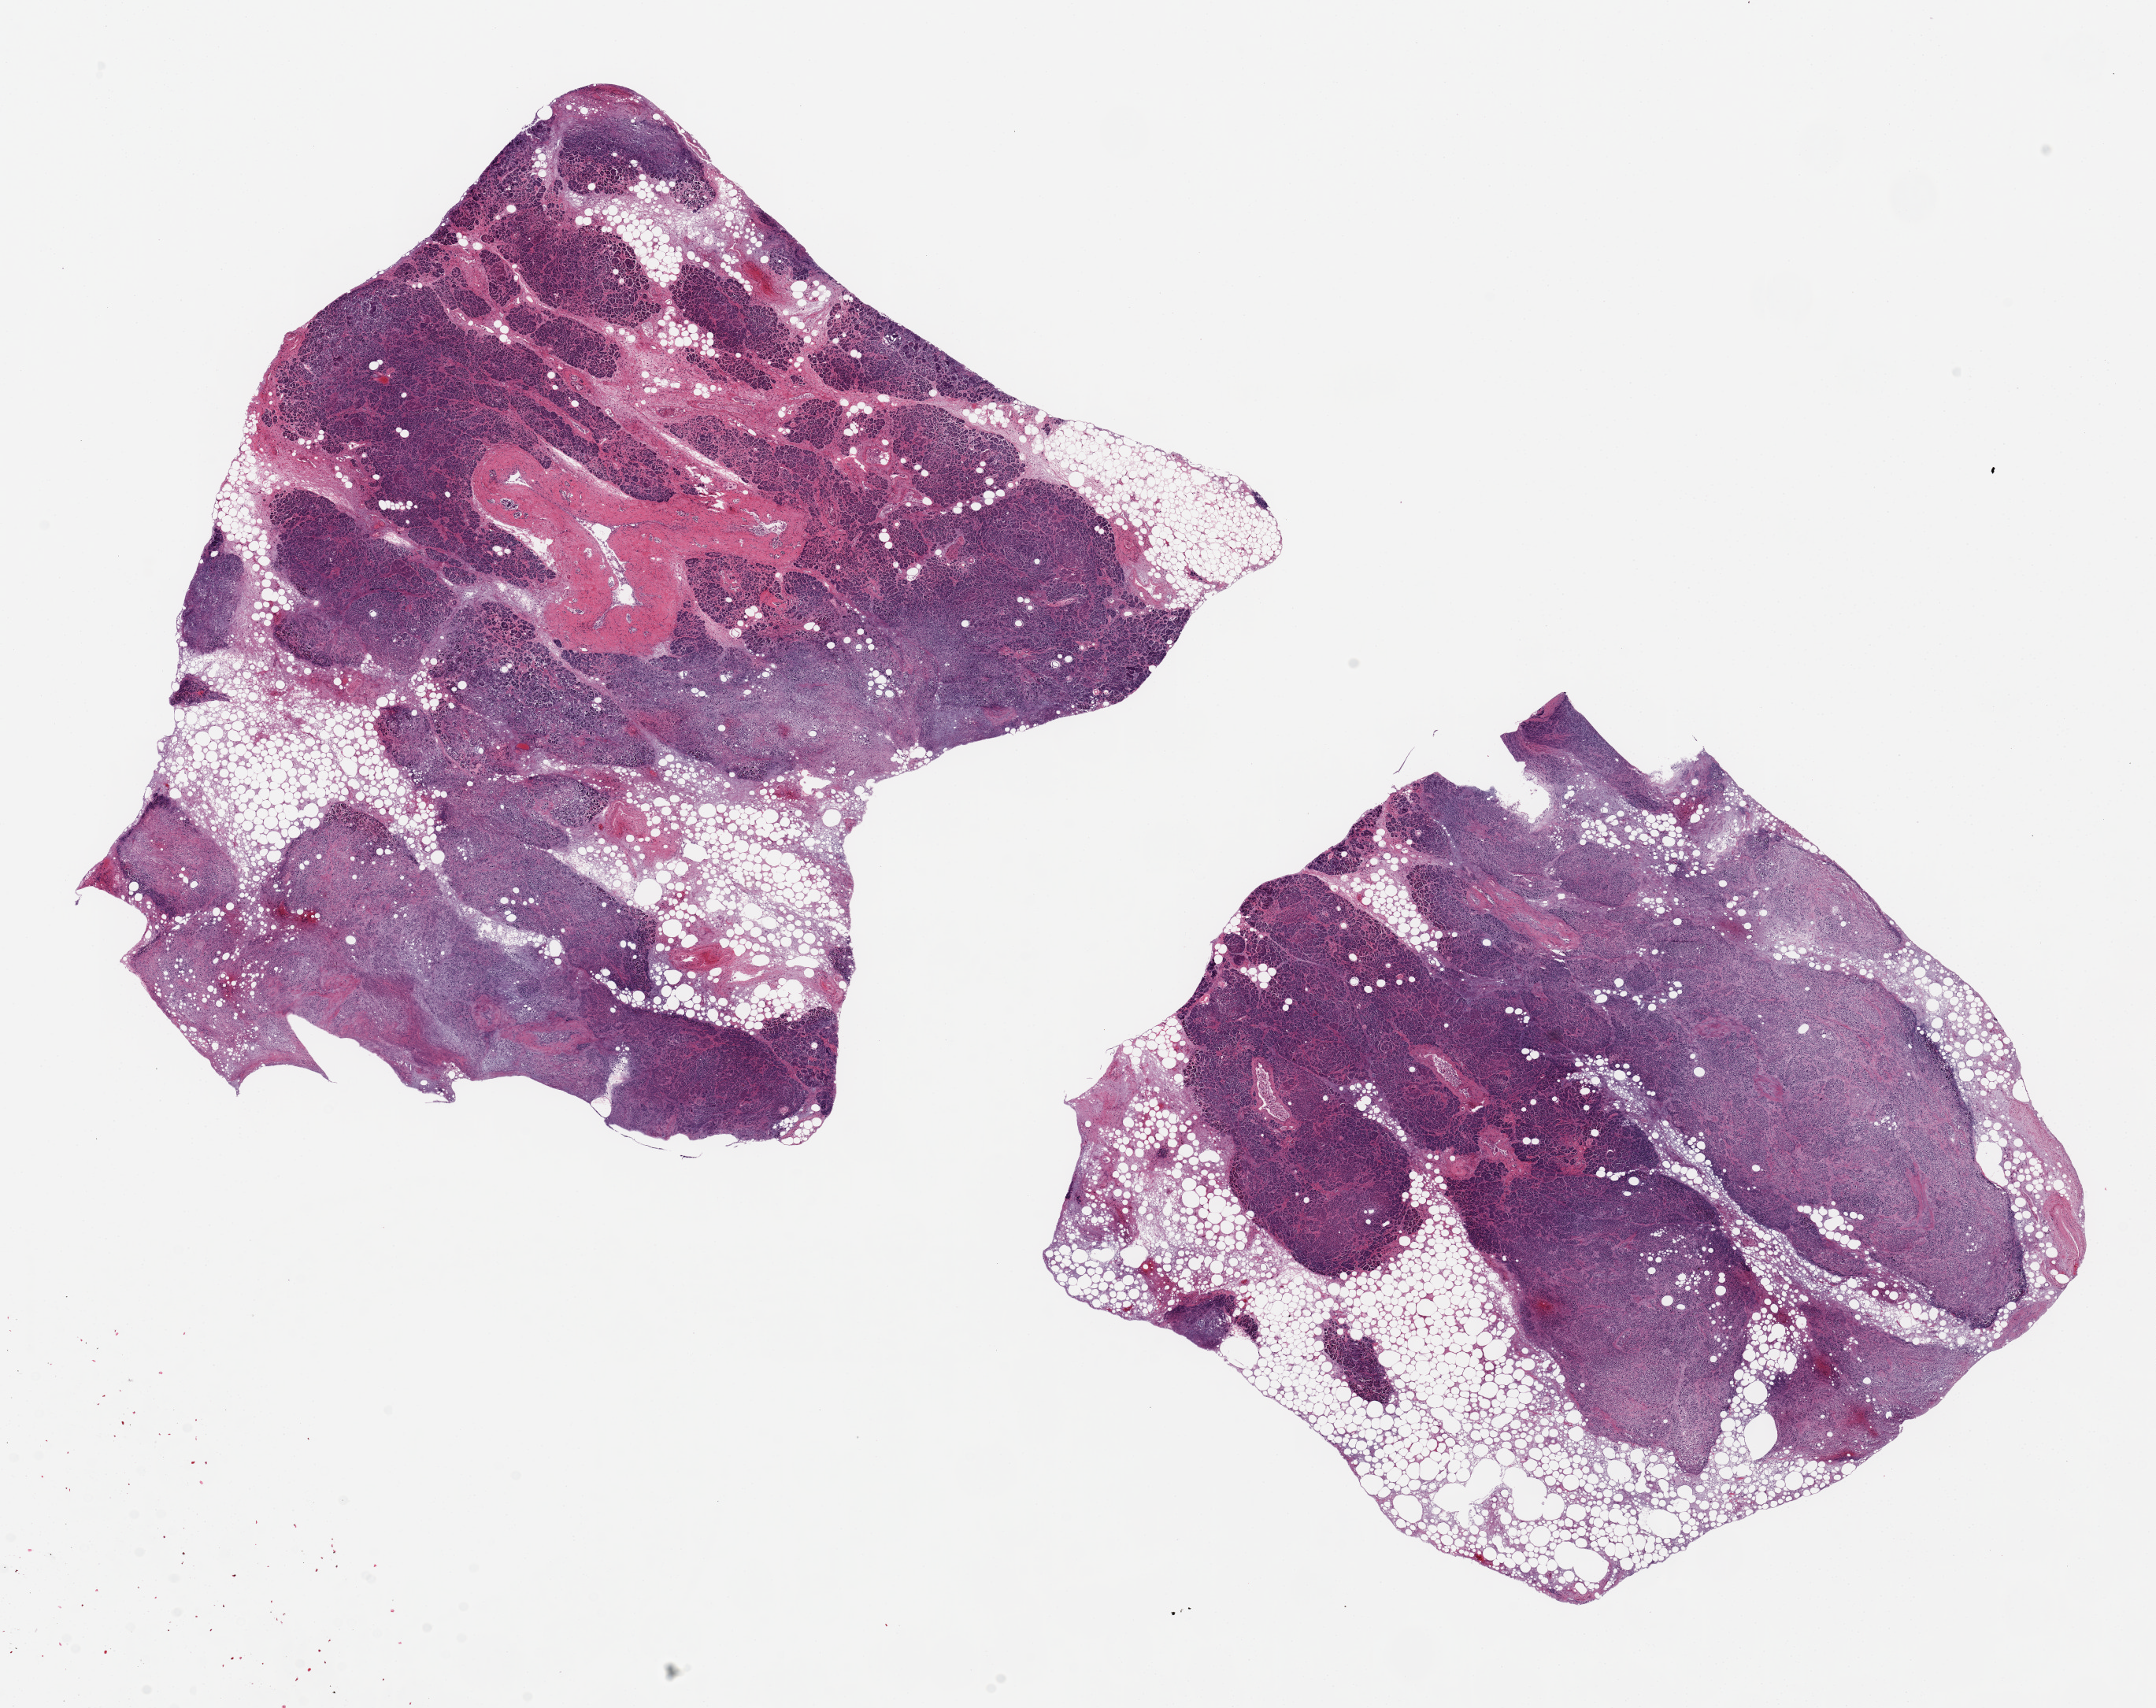
Whole-slide image, H&E stain — whole scanned area (about 21.7 x 17.2 mm, acquisition: 20x scan) shown as a low-resolution overview, PAXgene-fixed, paraffin-embedded tissue, sampled site (target tissue): pancreas, tissue donor sample. Donor: female.
Reviewer comment on this tissue sample: 2 ~8.5x8mm aliquots, extensive saponification of peripancreatic fat, ~25% of aliquots.